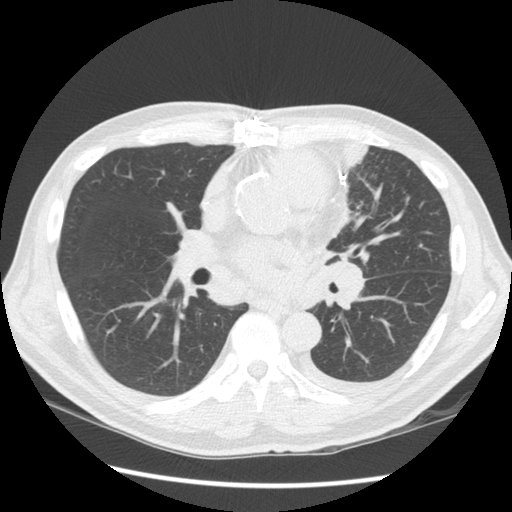
Low-dose screening chest CT, one axial slice. Position 75 of 136 along the scan axis. 120 kVp. Lung window (W 1500 / L -600 HU). 2.5 mm slice thickness. 512 × 512 image matrix.
Structures marked on this image (manually delineated by an expert):
- lesion 1 (tumor, upper lobe of left lung): bounding box [x1, y1, x2, y2] px = [329, 140, 368, 169]